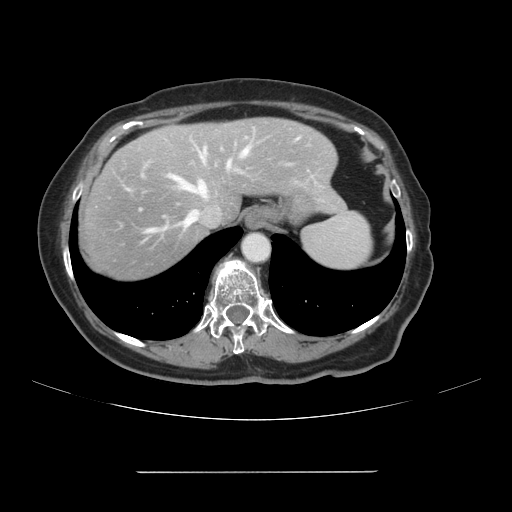
Contrast-enhanced abdominal CT, one axial slice; 120 kVp; soft-tissue window (W 400 / L 40 HU); 2.5 mm slice thickness; 512 × 512 image matrix, field of view 400 × 400 mm. Female patient, age 74 years. Case-level facts recorded for this patient, not image findings: diagnosis: colorectal cancer liver metastases, imaged before liver resection; multiple liver metastases: yes; largest metastasis: 1.1 cm; disease in both lobes: yes.
Annotated regions visible in this slice (outlined manually by an expert reader):
- hepatic veins: bounding box [x1, y1, x2, y2] px = [167, 138, 299, 226]
- liver: [77, 118, 344, 283]
- planned liver remnant (the part of the liver to remain after resection): [166, 118, 344, 219]
- portal vein (with intrahepatic branches): [185, 146, 250, 227]
- liver metastasis: [132, 190, 143, 199]